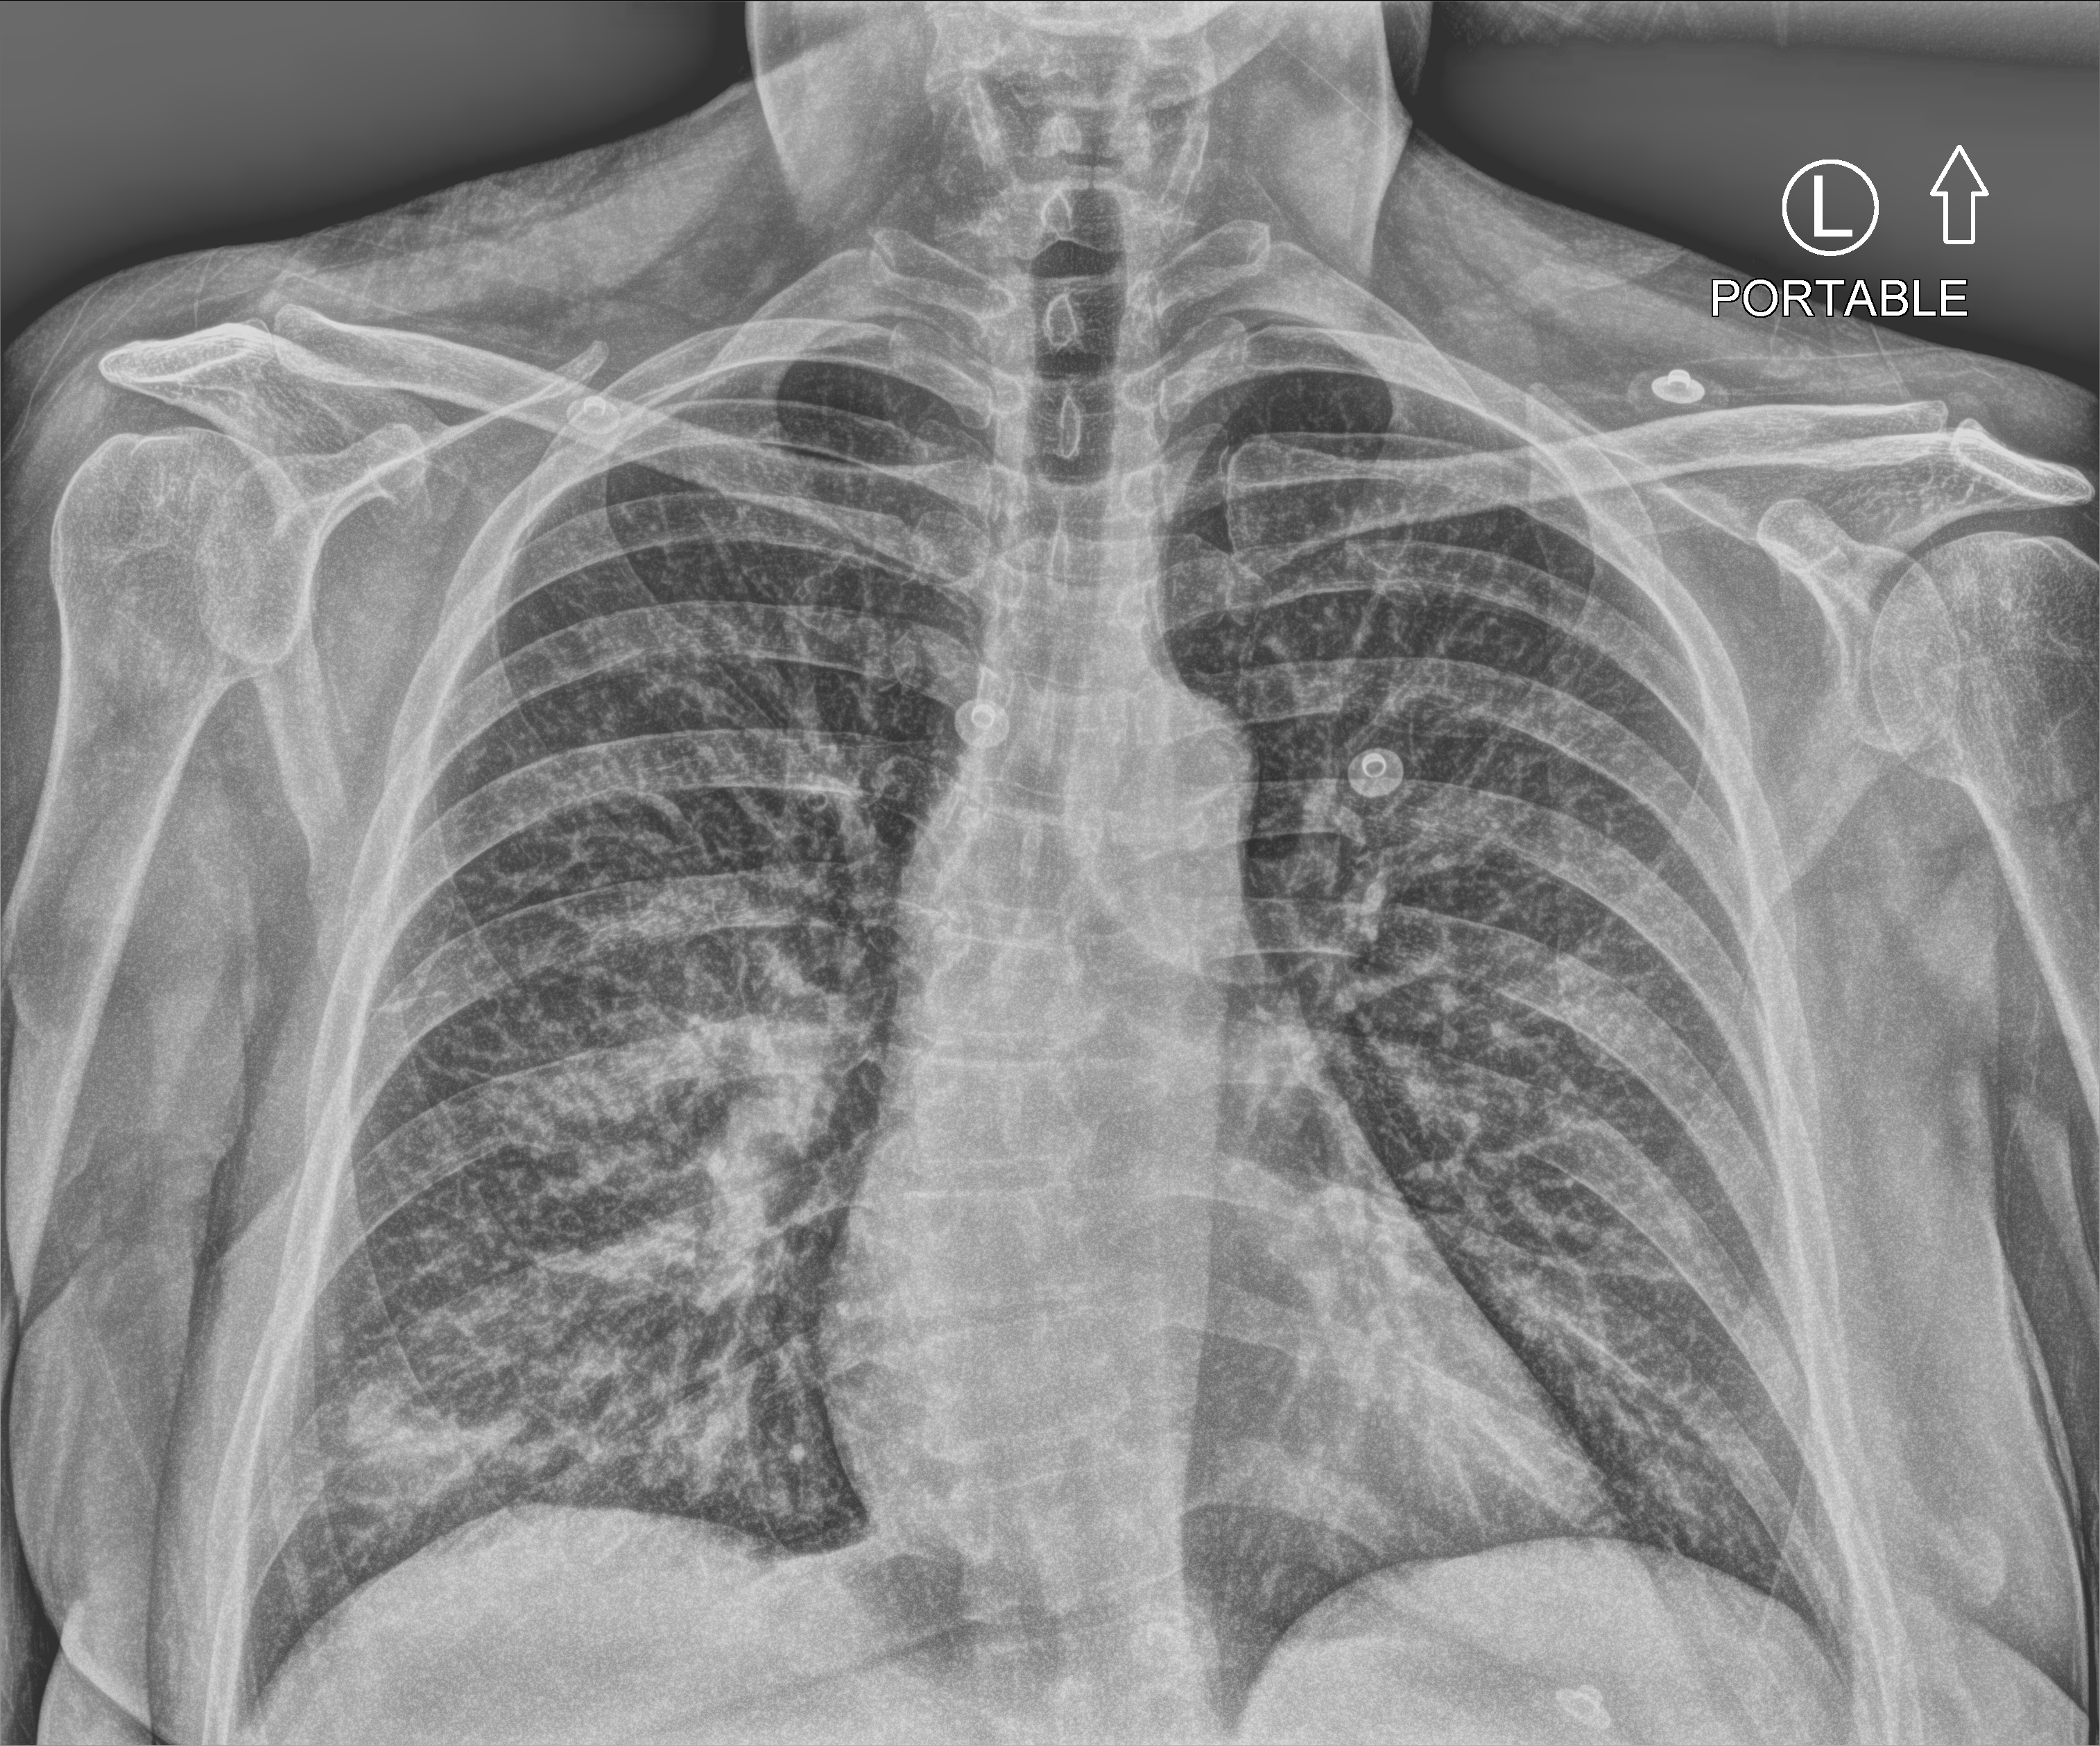
Bedside chest radiograph (computed radiography). Patient hospitalised with COVID-19; female, aged 18–59 years.
Admission-level facts for this patient (not findings on this image; timing relative to this image not recorded): length of hospital stay: 3 days; other chronic lung disease (admission record): no; chronic kidney disease (admission record): no.